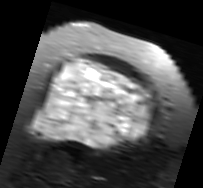
MRI of an extremity soft-tissue mass, one axial slice; slice 51 of 91 in the series (ordered by position); T2-weighted fat-saturated; MR volume resampled by the dataset authors to the PET/CT grid (not the native acquisition matrix); 3.27 mm slice thickness; 203 × 188 image matrix. Female patient. Case-level facts recorded for this patient, not image findings: histological type: malignant solitary fibrous tumor; grade: intermediate; site of the primary tumour: right thigh.
Outlined on this slice (expert contour drawn on MRI and transferred to this co-registered scan by the dataset authors):
- gross tumour volume including surrounding oedema: bounding box (x1, y1, x2, y2) in pixels: (30, 58, 155, 150)
- gross tumour volume (mass): (33, 58, 152, 148)